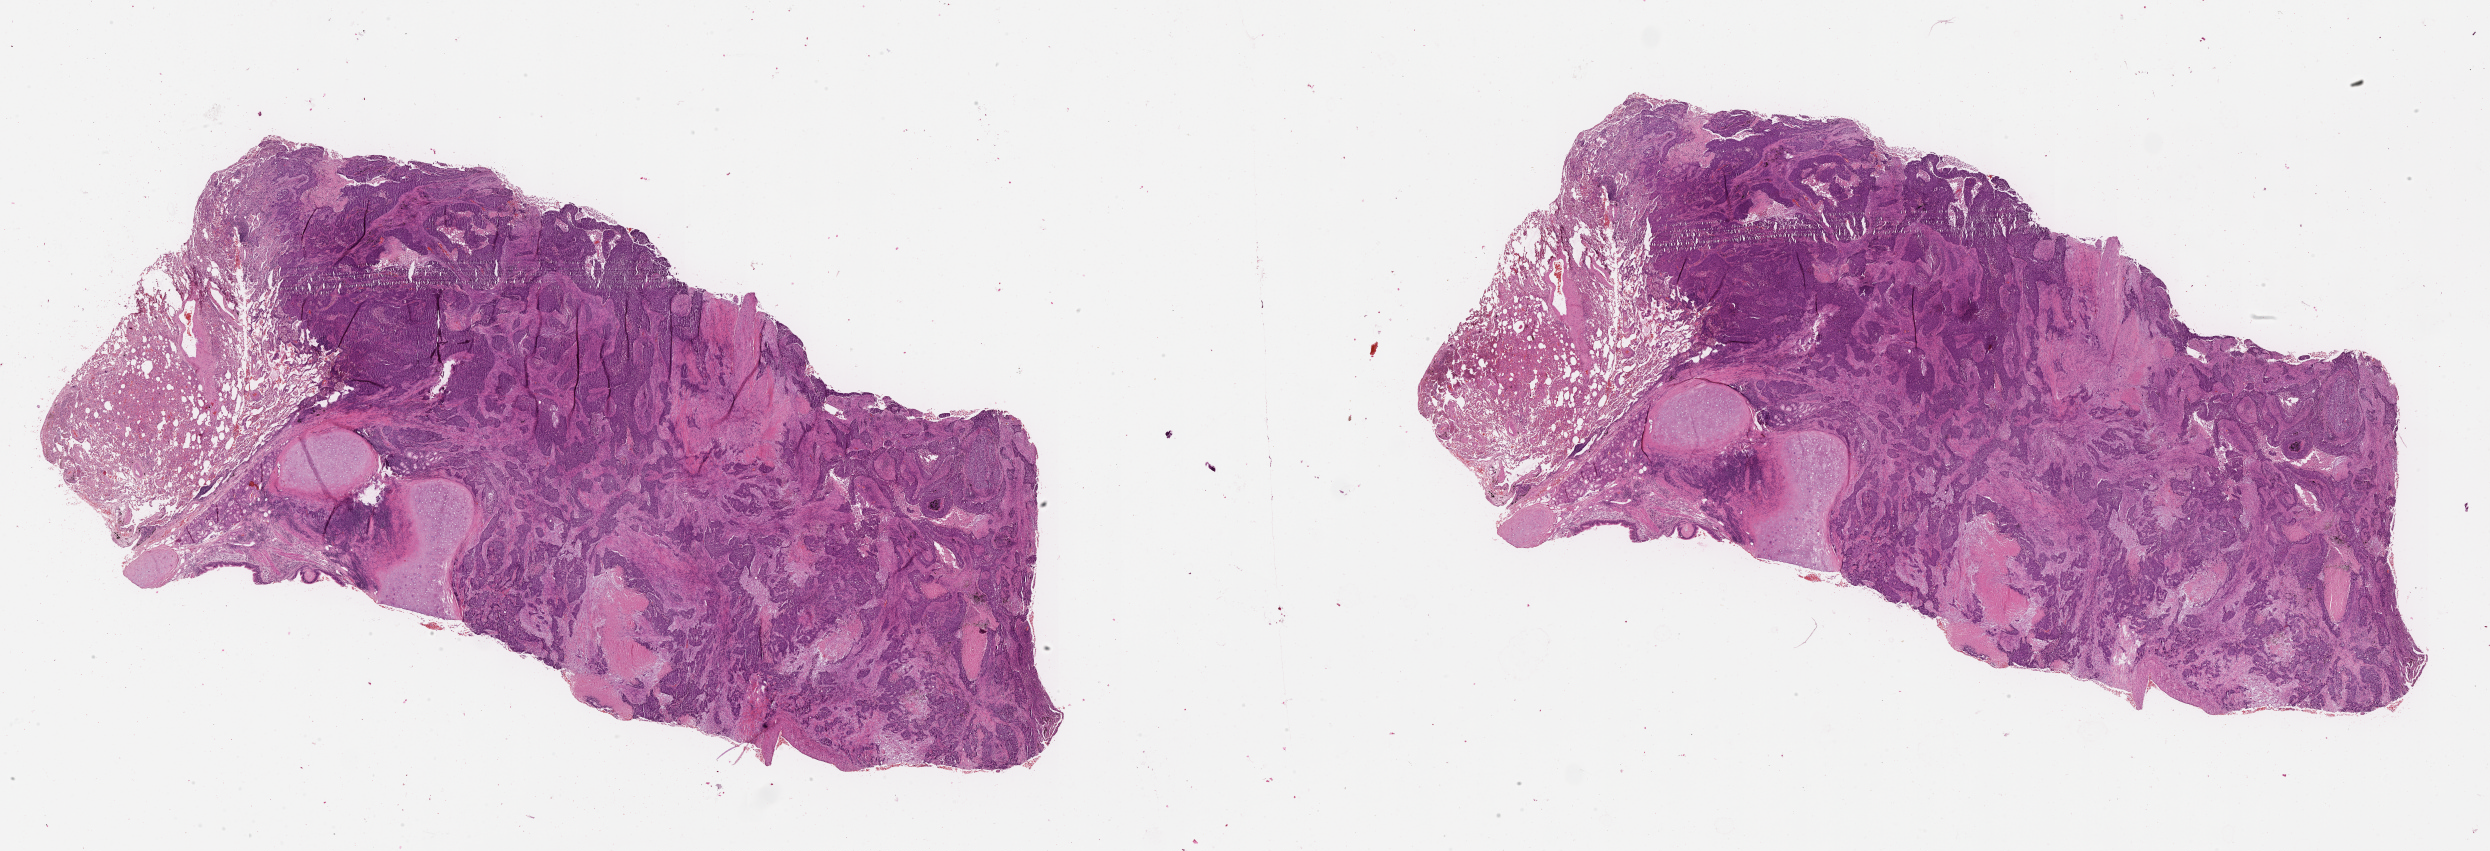
Digitized H&E tissue section (whole slide), a low-resolution overview of the entire scanned area, about 40.1 x 13.7 mm (slide scanned at 20x), lung, tumour tissue. Male, 59 y/o.
Patient diagnosis (cohort enrolment): squamous cell carcinoma (lung).